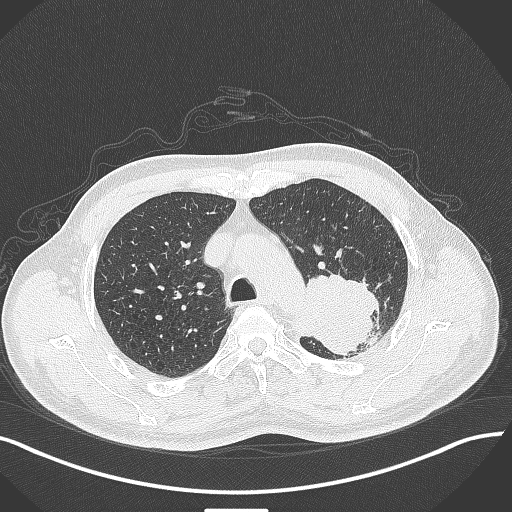
Chest CT, one axial slice. Position 316 of 429 along the scan axis. 120 kVp. Lung window (W 1500 / L -600 HU). 1 mm slice thickness. 512 × 512 image matrix, field of view 400 × 400 mm. Male patient, age 55 years. Case-level facts recorded for this patient, not image findings: clinical TNM (as recorded): T3 N0 M1c; histopathological grade: G3.
Structures marked on this image (bounding box drawn by a radiologist):
- lung tumour (recorded histology: adenocarcinoma): bounding box <295,271,383,361> (left, top, right, bottom; pixels)